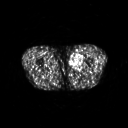
FDG PET of an extremity soft-tissue mass (from a PET/CT study), one axial slice. Slice 245 of 311 in the series (ordered by position). 3.27 mm slice thickness. 128 × 128 image matrix, field of view 500 × 500 mm. Male patient, age 29 years. Case-level facts recorded for this patient, not image findings: histological type: mixoid liposarcoma; grade: low; site of the primary tumour: left thigh.
Outlined on this slice (expert contour drawn on MRI and transferred to this co-registered scan by the dataset authors):
- gross tumour volume (mass): bounding box <69,53,83,69> (left, top, right, bottom; pixels)